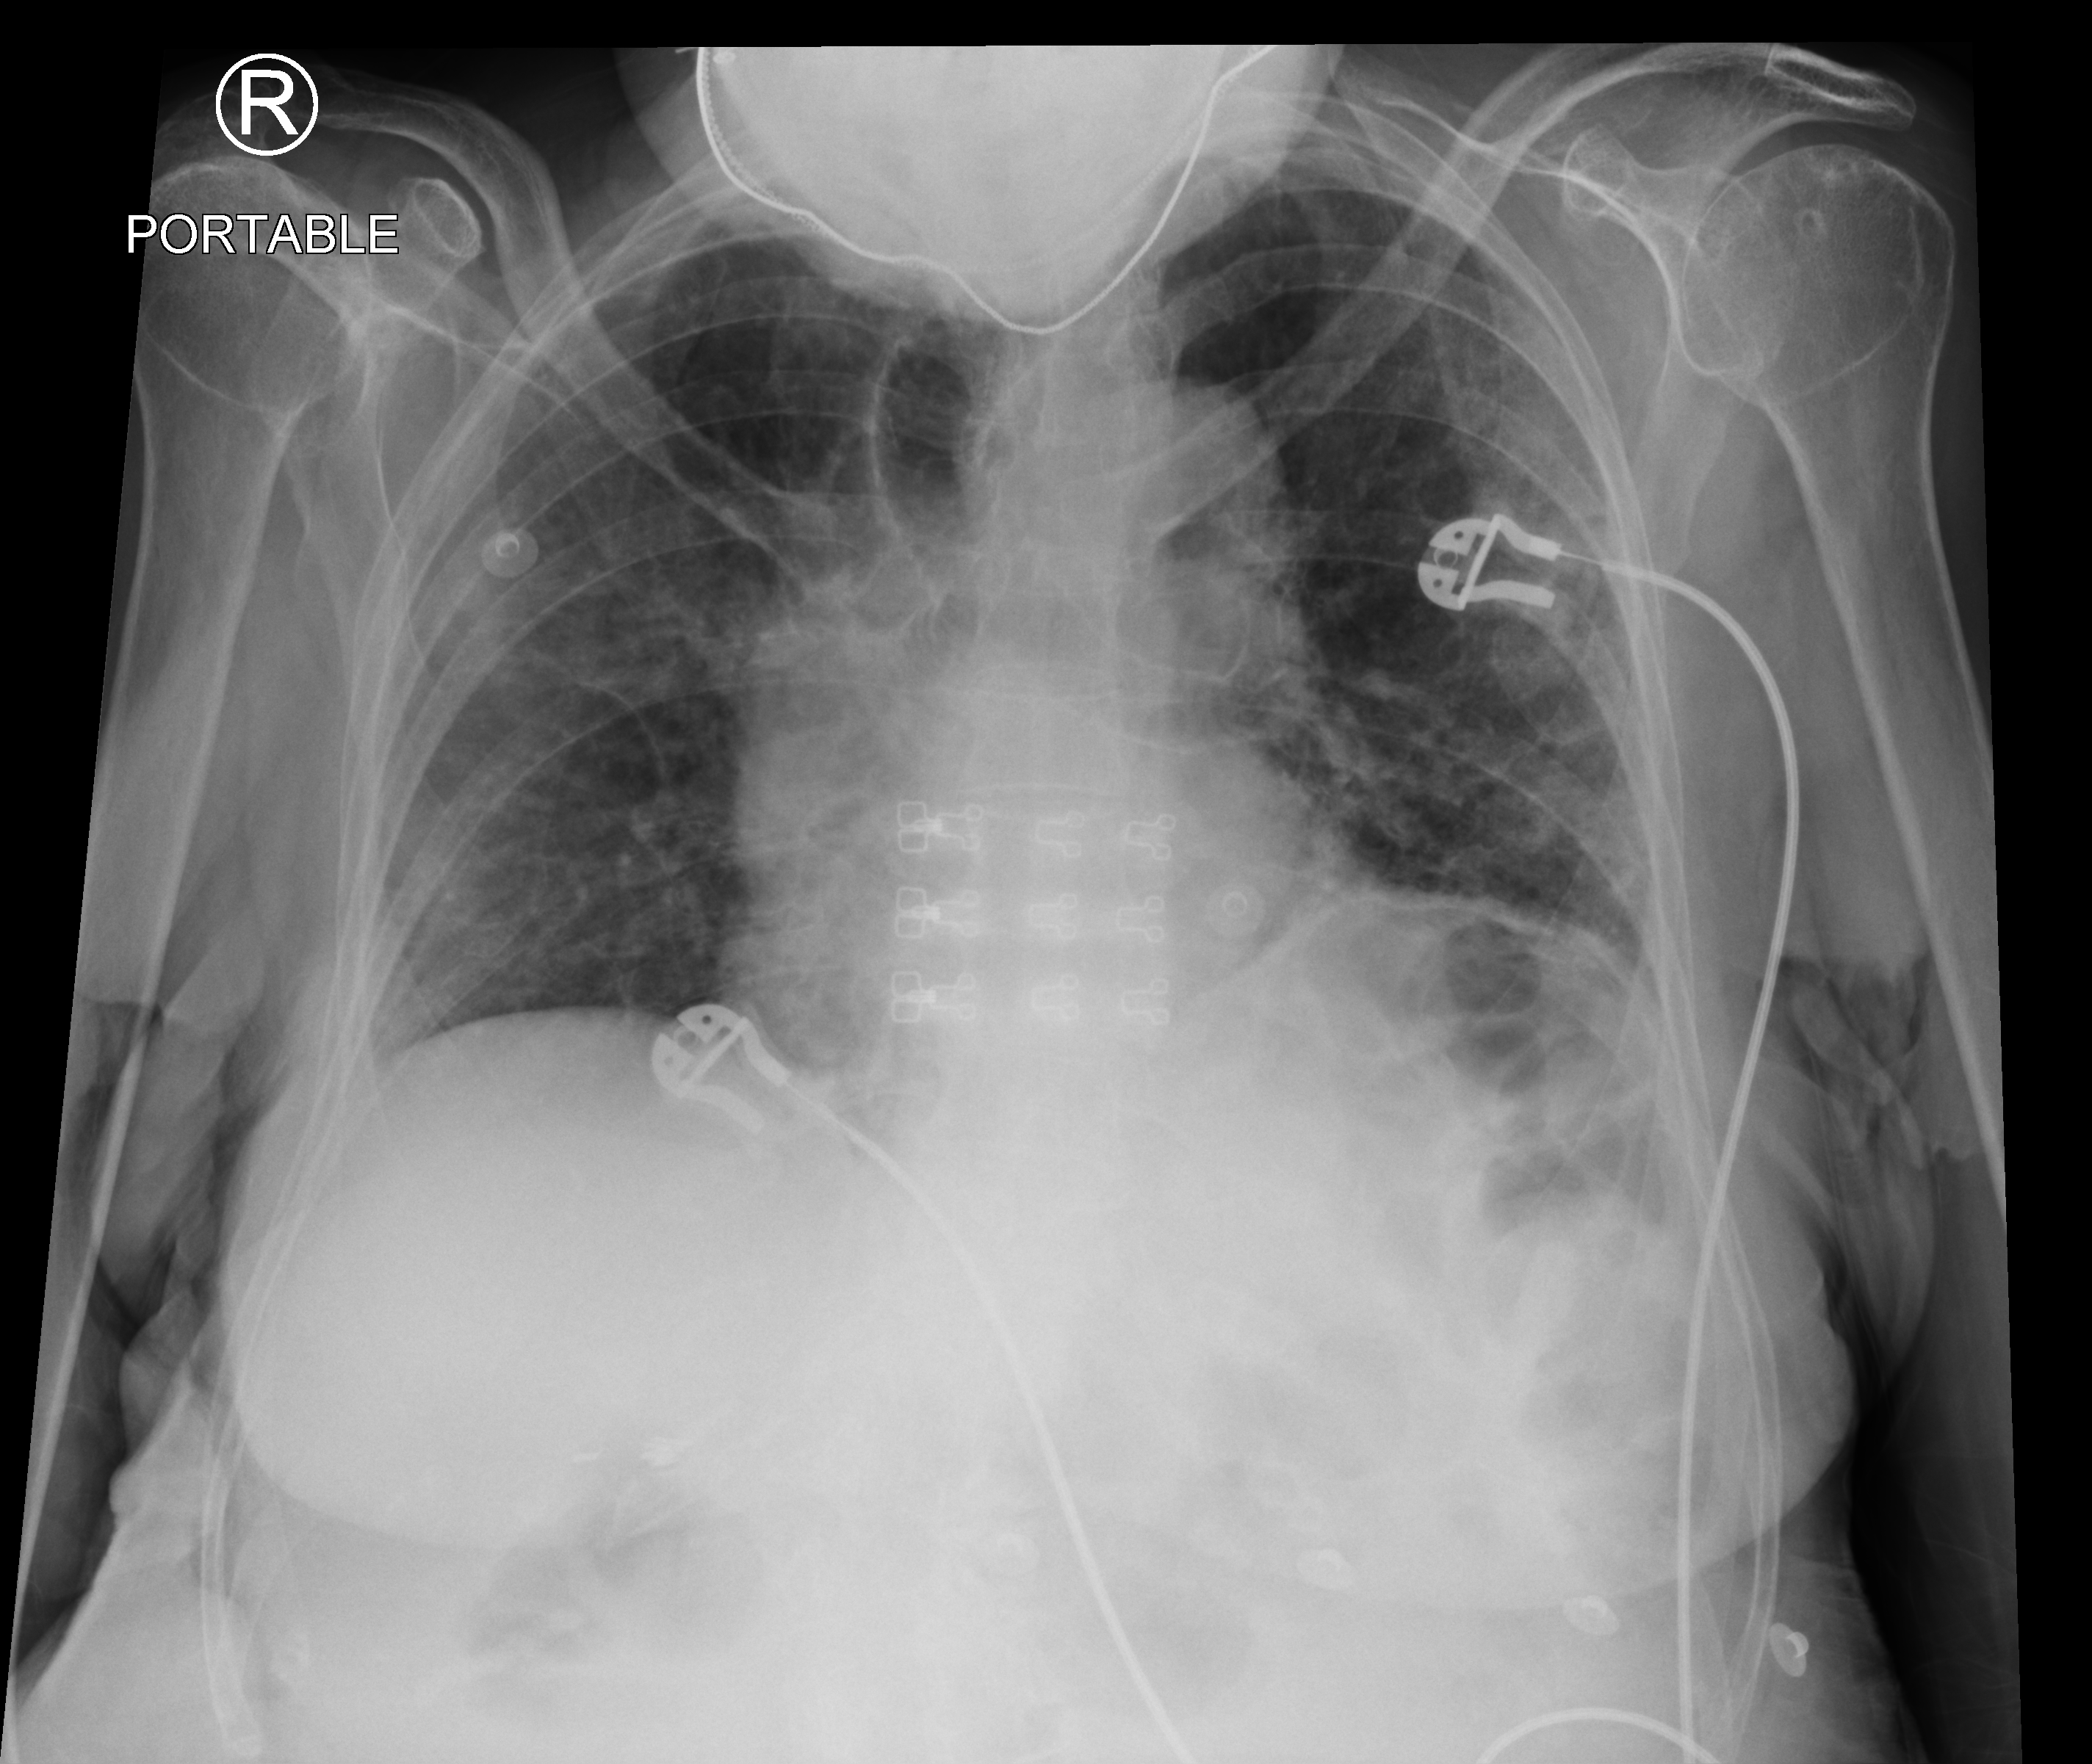
Bedside chest radiograph (computed radiography), anteroposterior (AP) projection. Female patient hospitalised with COVID-19, age 75–90 years.
Admission-level facts for this patient (not findings on this image; timing relative to this image not recorded): mechanically ventilated during this hospital stay: no; admitted to intensive care during this hospital stay: no; length of hospital stay: 1 day.